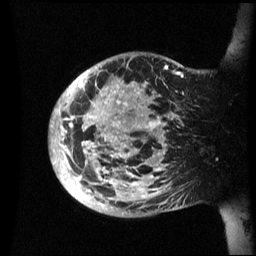
Breast MRI (dynamic contrast-enhanced), one sagittal slice. Dynamic contrast-enhanced series, image 2 of 3 at this slice position (ordered by acquisition). 1.5 T. TE 4.2 ms, TR 8.4 ms. 2.4 mm slice thickness. 256 × 256 image matrix, field of view 230 × 230 mm. Patient: female, 48 years.
Annotated regions visible in this slice (semi-automatically segmented with operator editing):
- analysis volume of interest (the breast-tissue region the enhancement analysis was run in; not a lesion): box from (x=49, y=52) to (x=200, y=217) px
- tumour enhancement mask (voxels above the 70 % enhancement threshold inside the analysis volume of interest): (x=49, y=65)–(x=184, y=205)